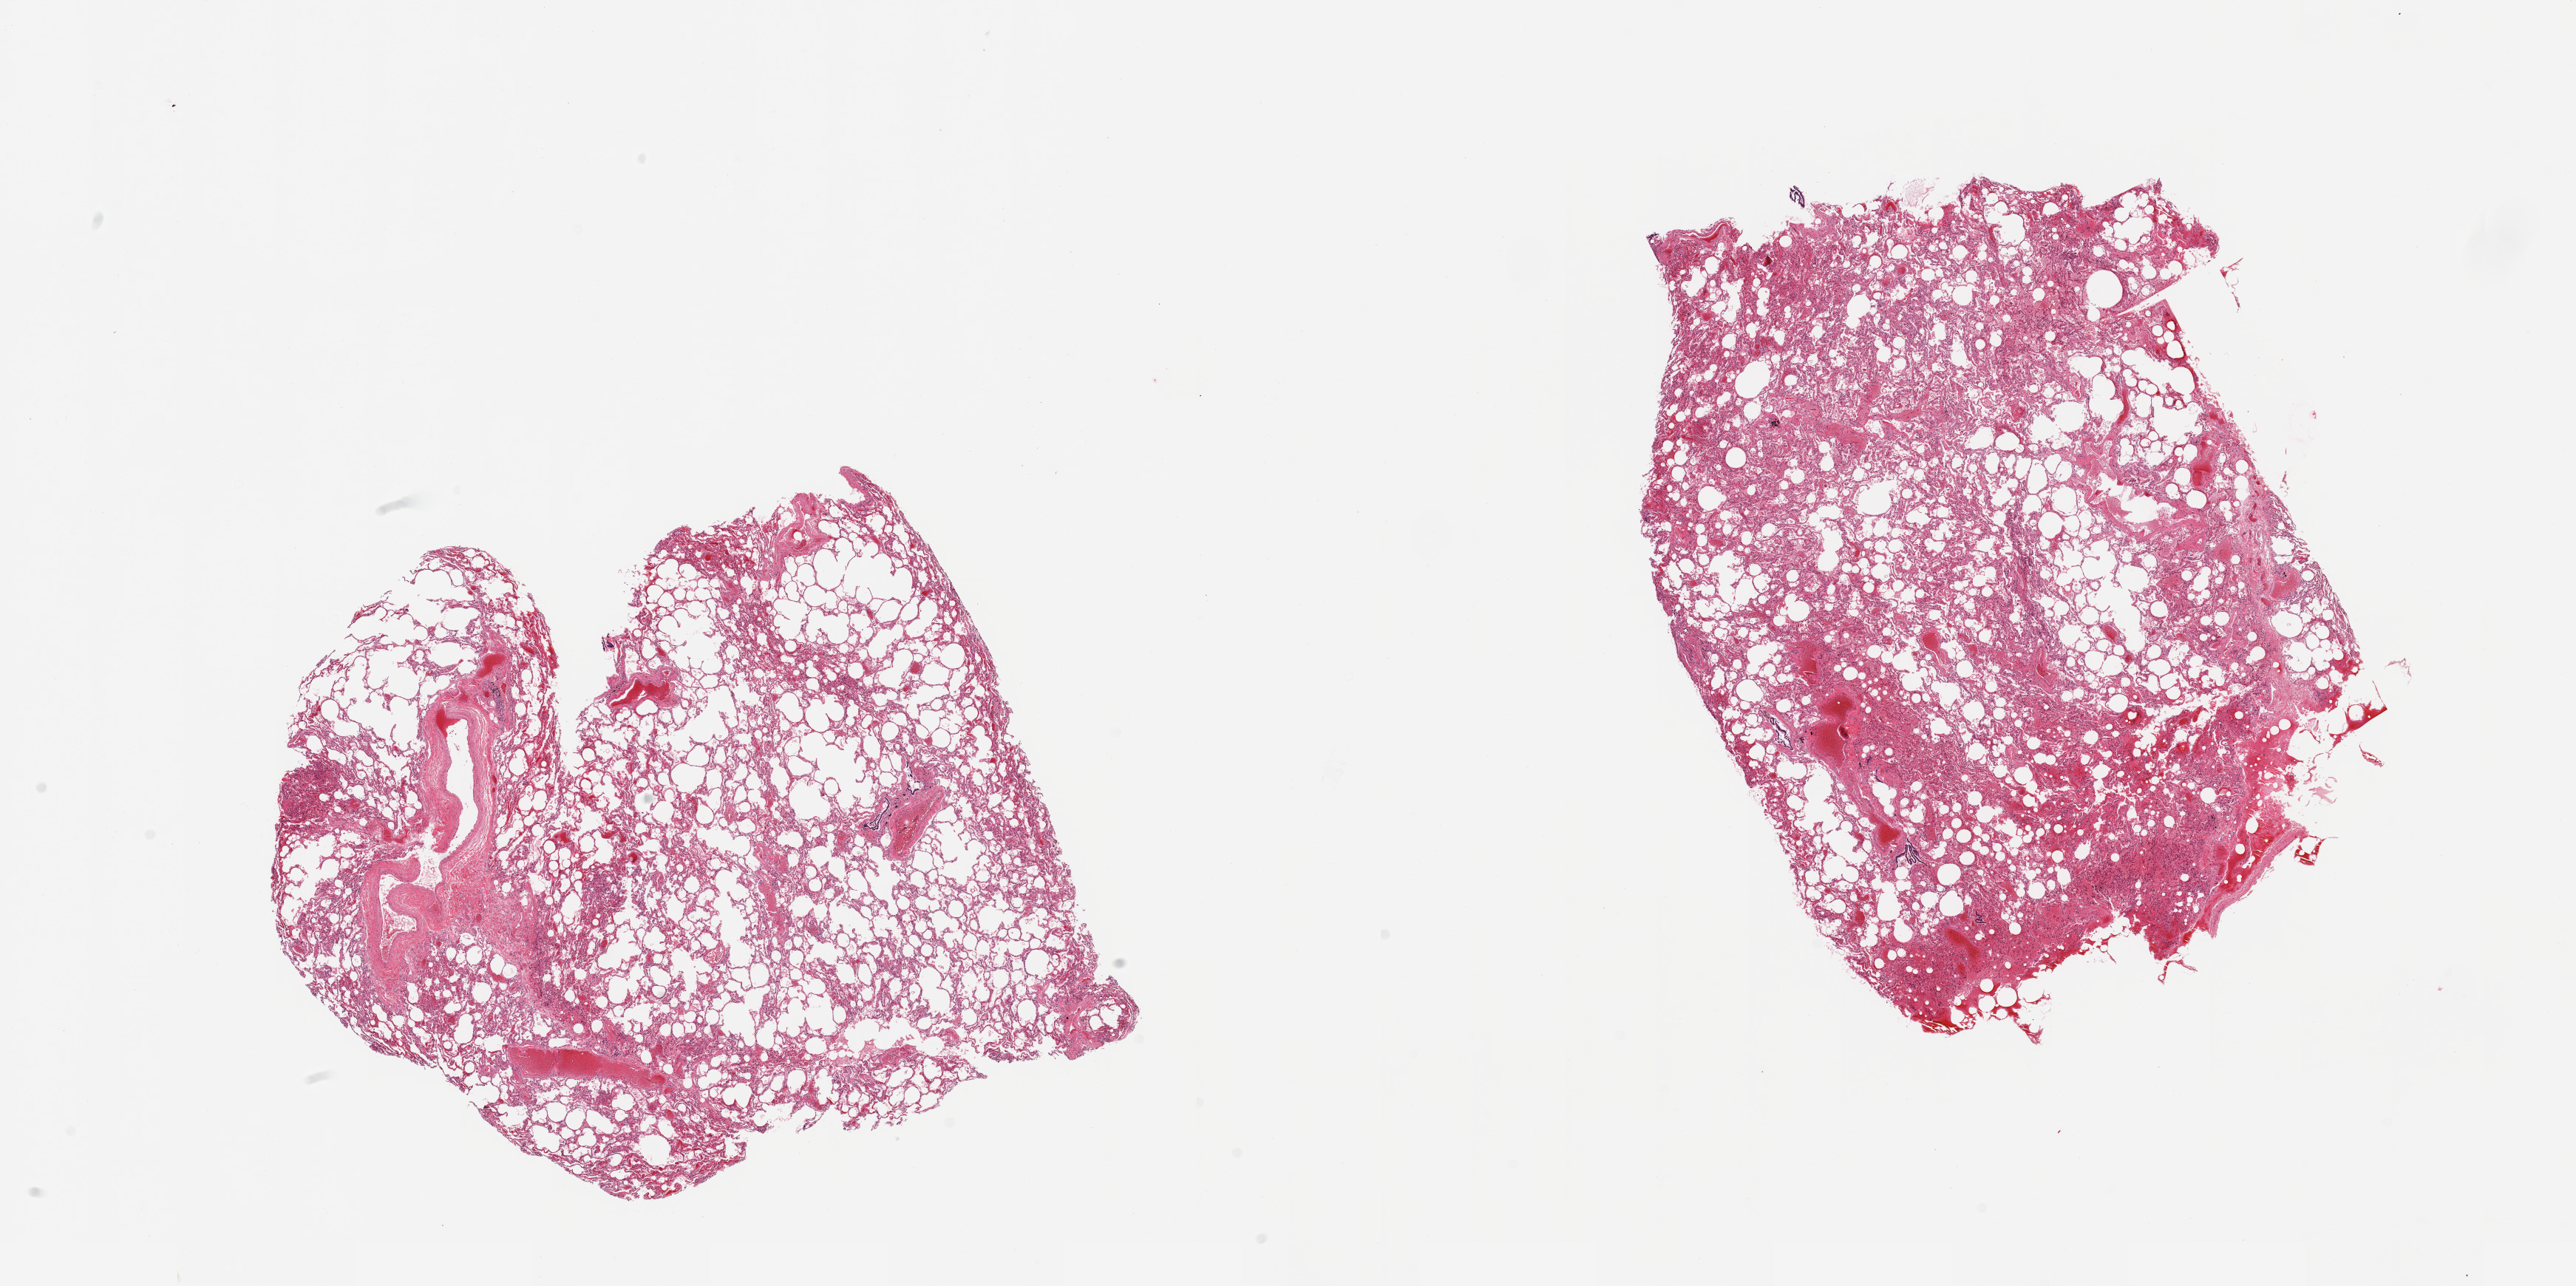
Whole-slide image, haematoxylin and eosin stain — whole scanned area (about 27.6 x 13.8 mm) shown as a low-resolution overview. PAXgene-fixed paraffin-embedded (PFPE) section. Sampled site (target tissue): lung. Donor tissue sample. Male donor.
Reviewer comment on this tissue sample: 2 pieces, patchy, moderate congestion.